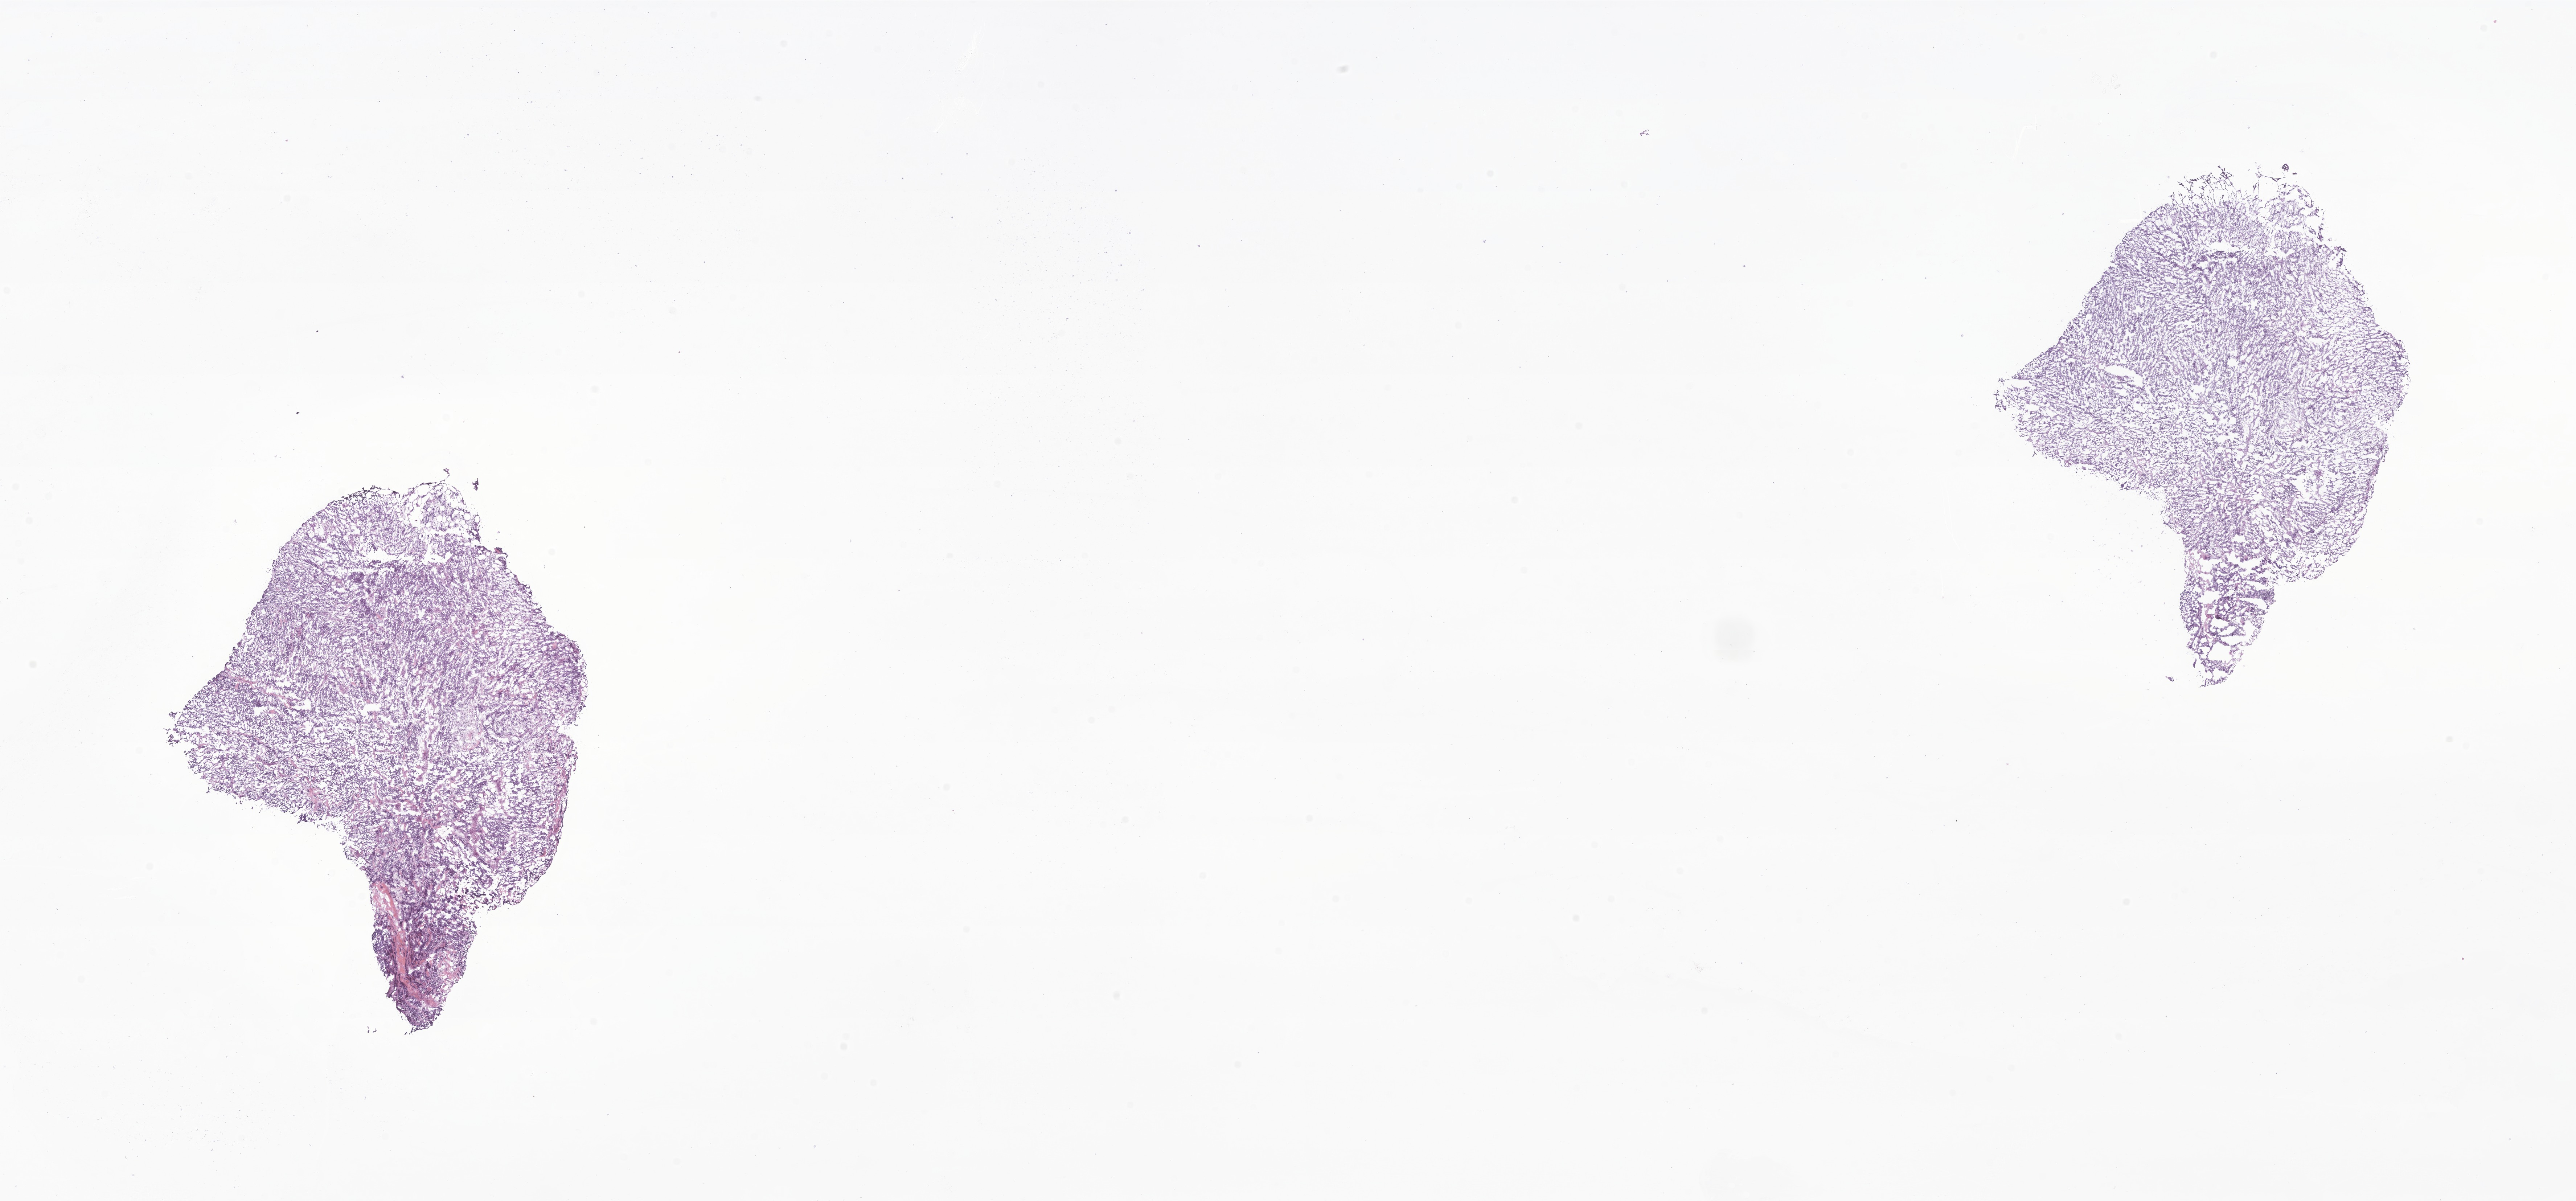
H&E whole-slide image of tumor tissue from the upper limb, shown as a low-resolution overview of the whole scanned area (about 29.9 x 14.0 mm), frozen section. Male patient, age 151 months (12 years 7 months).
Diagnosis: Alveolar rhabdomyosarcoma.